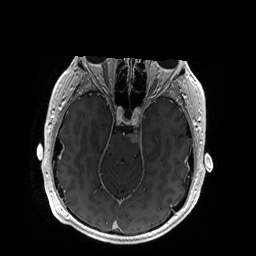
Brain MRI from a brain-tumour surgery series, one axial slice. T1-weighted post-contrast. 256 × 256 image matrix, field of view 256 × 256 mm. From the clinical record (not read from this slice): histopathology: Glioblastoma; WHO grade: 4; IDH mutation: no.
Structures marked on this image (manually delineated by an expert):
- tumour: box from (x=130, y=127) to (x=143, y=145) px